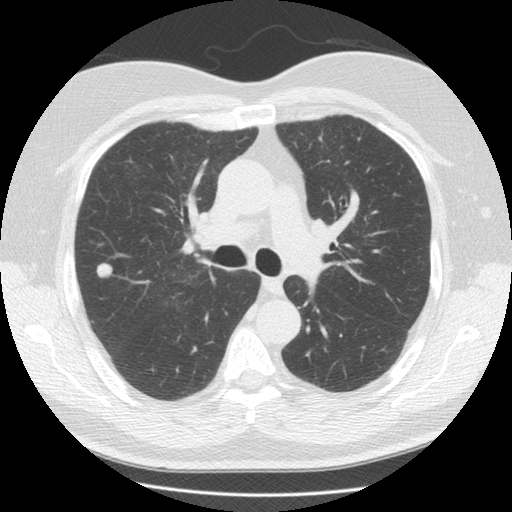
Low-dose screening chest CT, one axial slice; reconstruction kernel STANDARD; lung window (W 1500 / L -600 HU); 512 × 512 image matrix, field of view 350 × 350 mm.
Outlined on this slice (expert manual segmentation):
- lesion 1 (tumor, upper lobe of right lung): bounding box [x1, y1, x2, y2] px = [96, 263, 113, 278]